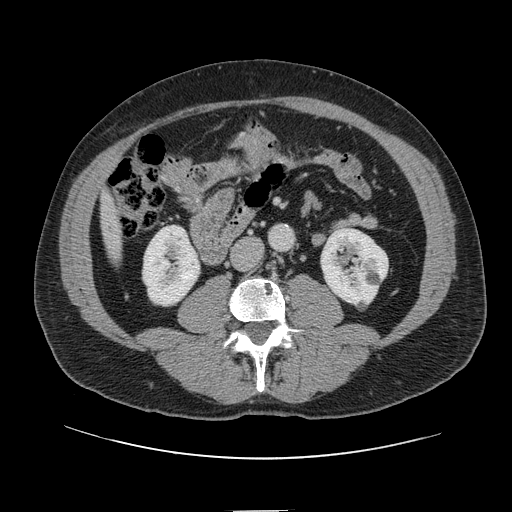
Contrast-enhanced abdominal CT, one axial slice. Position 12 of 161 along the scan axis. Intravenous contrast given. Soft-tissue window (W 400 / L 40 HU). 2.5 mm slice thickness. 512 × 512 image matrix, field of view 412 × 412 mm. Male patient, age 66 years. Case-level facts recorded for this patient, not image findings: diagnosis: colorectal cancer liver metastases, imaged before liver resection; multiple liver metastases: no; largest metastasis: 3.5 cm; disease in both lobes: no.
Structures marked on this image (outlined manually by an expert reader):
- liver: bounding box <103,197,121,260> (left, top, right, bottom; pixels)
- planned liver remnant (the part of the liver to remain after resection): <103,198,118,238>